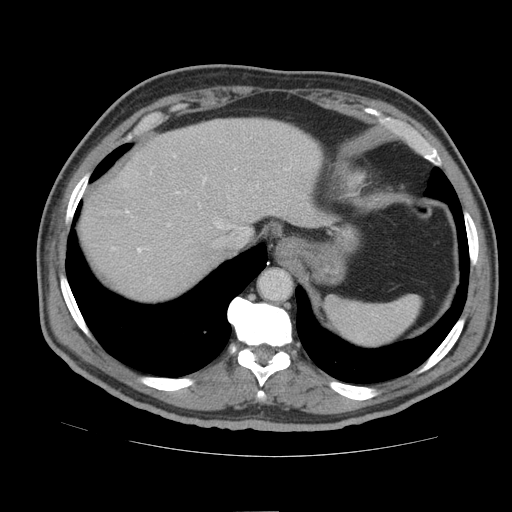
Contrast-enhanced abdominal CT (liver protocol), one axial slice; slice 72 of 105 in the series (ordered by position); soft-tissue window (W 400 / L 40 HU); 2.5 mm slice thickness; 512 × 512 image matrix, field of view 380 × 380 mm. From the clinical record (not read from this slice): diagnosis: hepatocellular carcinoma (patient treated with transarterial chemoembolisation; whether this scan precedes or follows treatment is not stated here); TNM stage (as recorded): Stage-IIIB; Child-Pugh class: A; tumour nodularity: multinodular.
Outlined on this slice (semi-automatic segmentation, software-assisted and operator-edited):
- abdominal aorta: box from (x=260, y=270) to (x=291, y=300) px
- liver parenchyma outside the tumour (the mass and vessels are separate outlines, so this box may not span the whole liver): (x=80, y=118)–(x=331, y=298)
- liver vessels: (x=127, y=181)–(x=204, y=253)